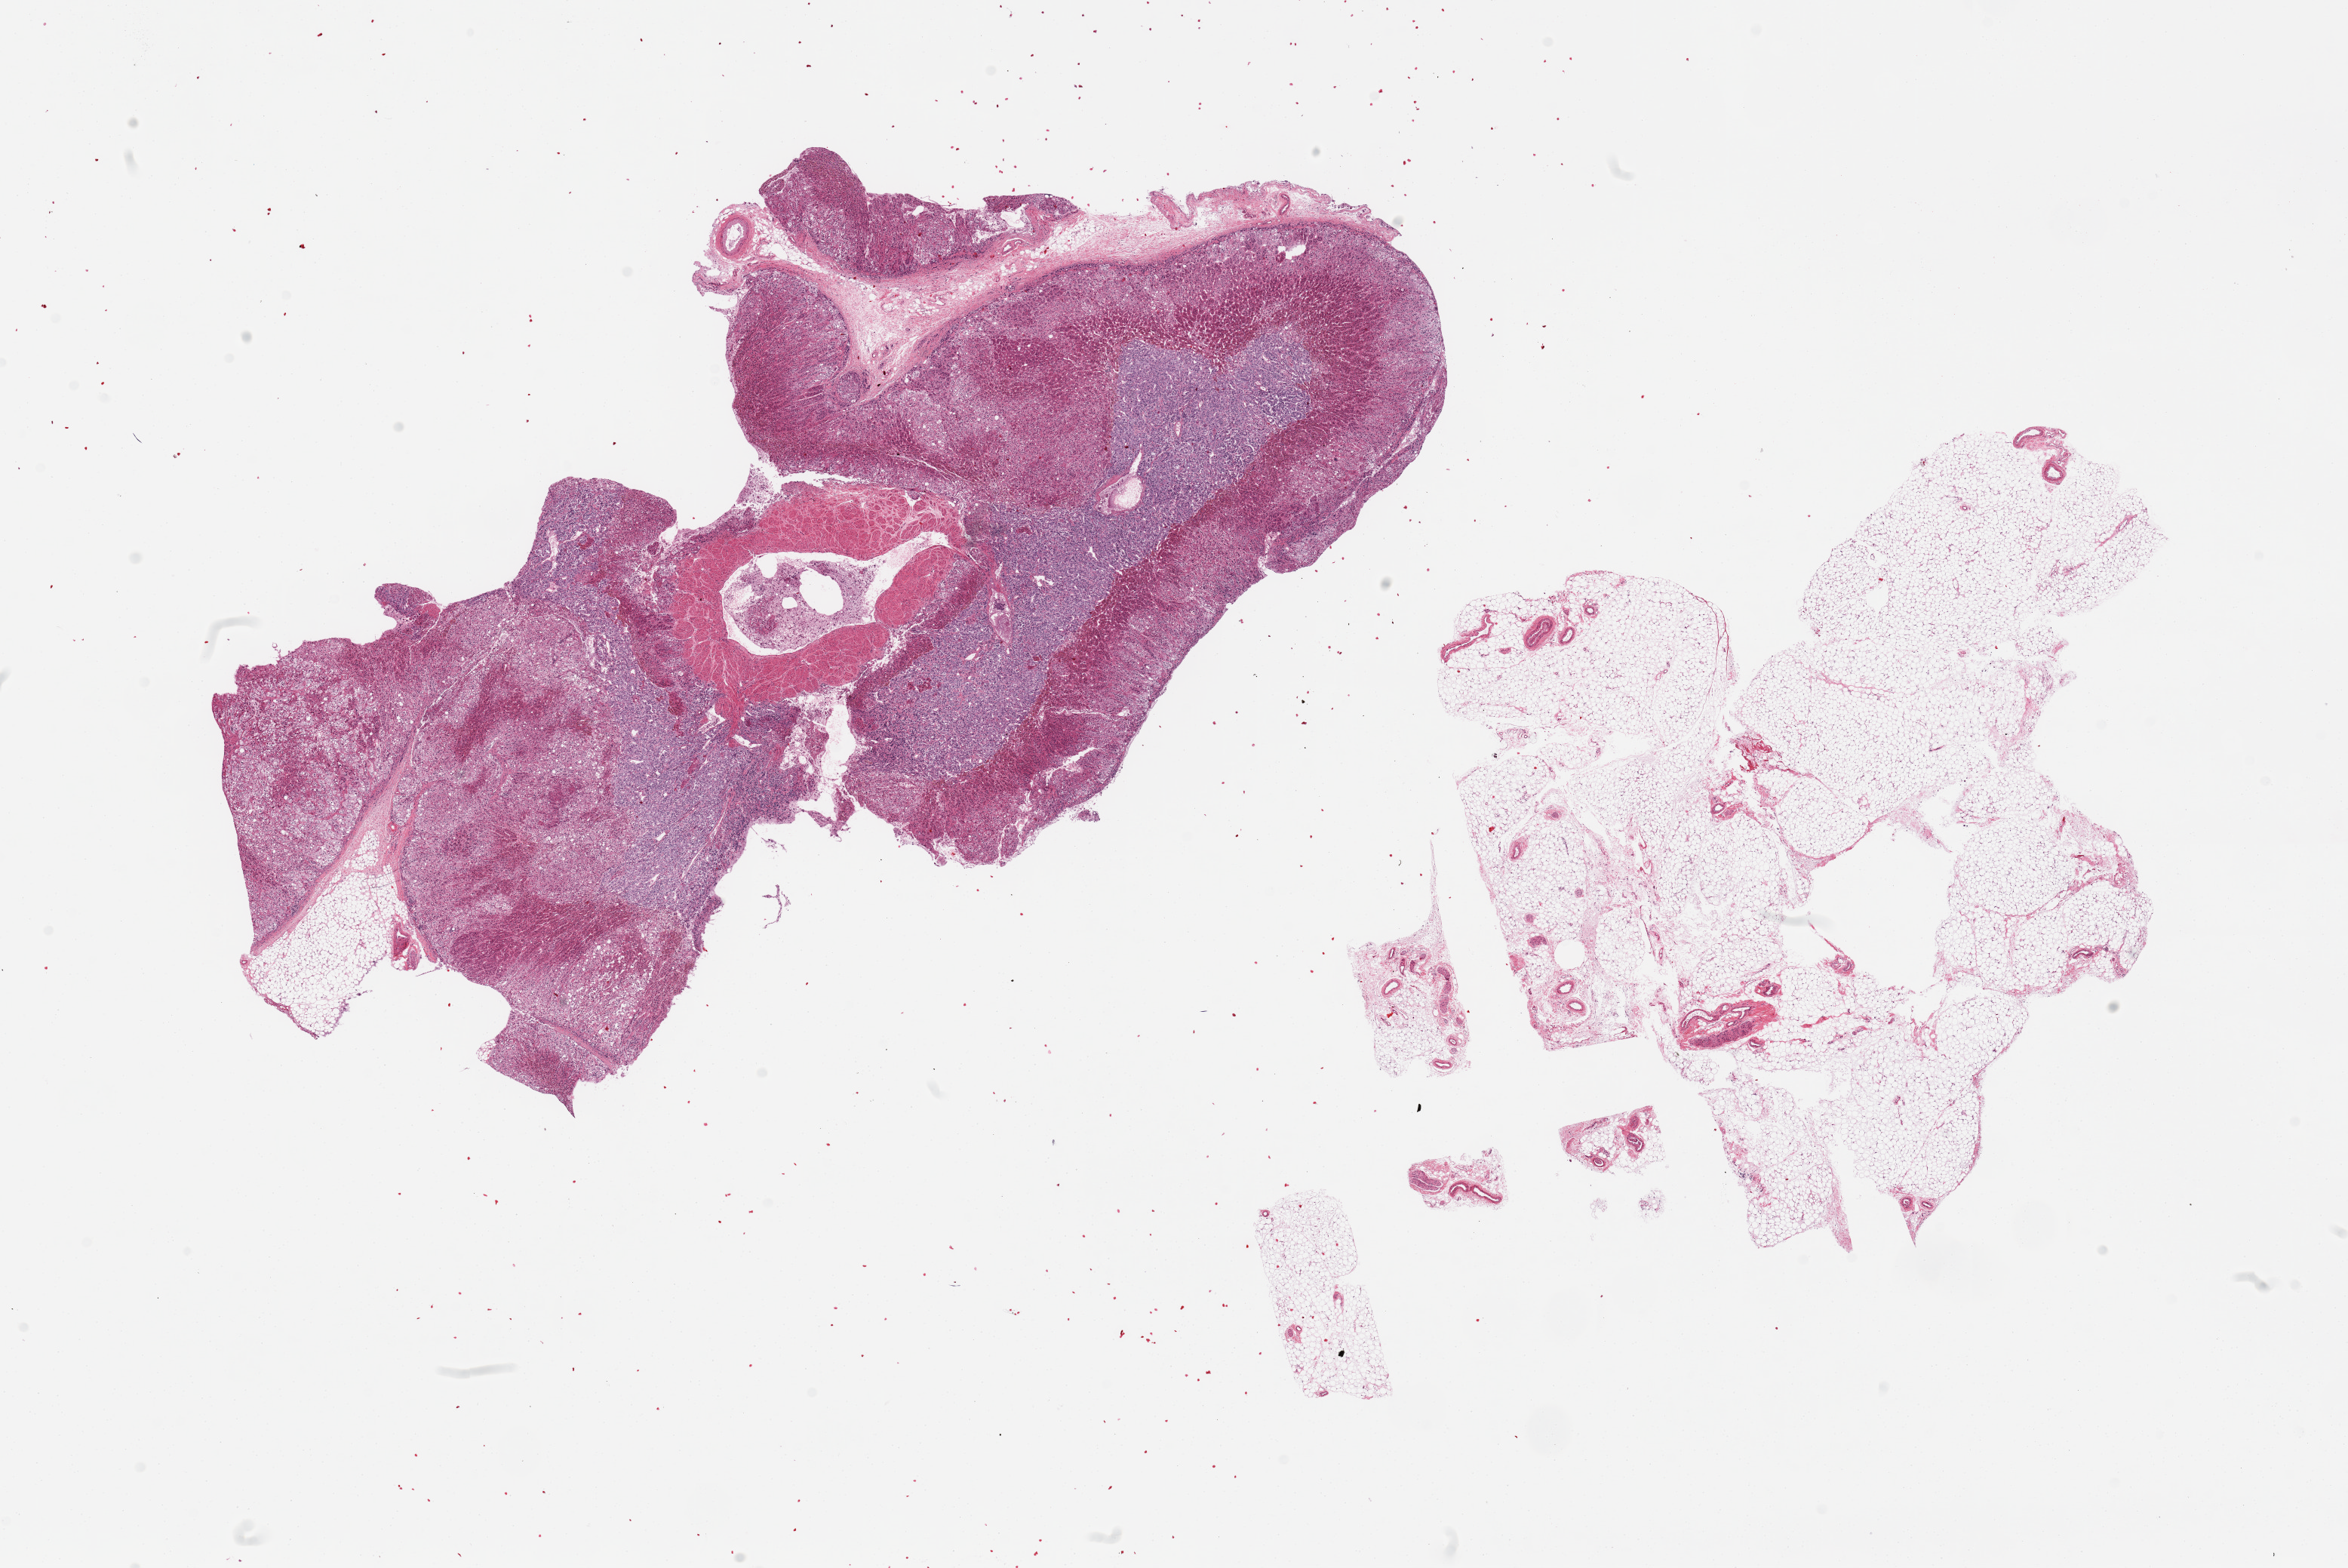
Whole-slide image, haematoxylin and eosin stain — a low-resolution overview of the entire scanned area, about 24.6 x 16.4 mm. PAXgene-fixed, paraffin-embedded tissue. Target tissue: adrenal gland. Donor tissue sample. Male donor.
* reviewer comment on this tissue sample: 2 pieces, one piece is fat, one is adrenal